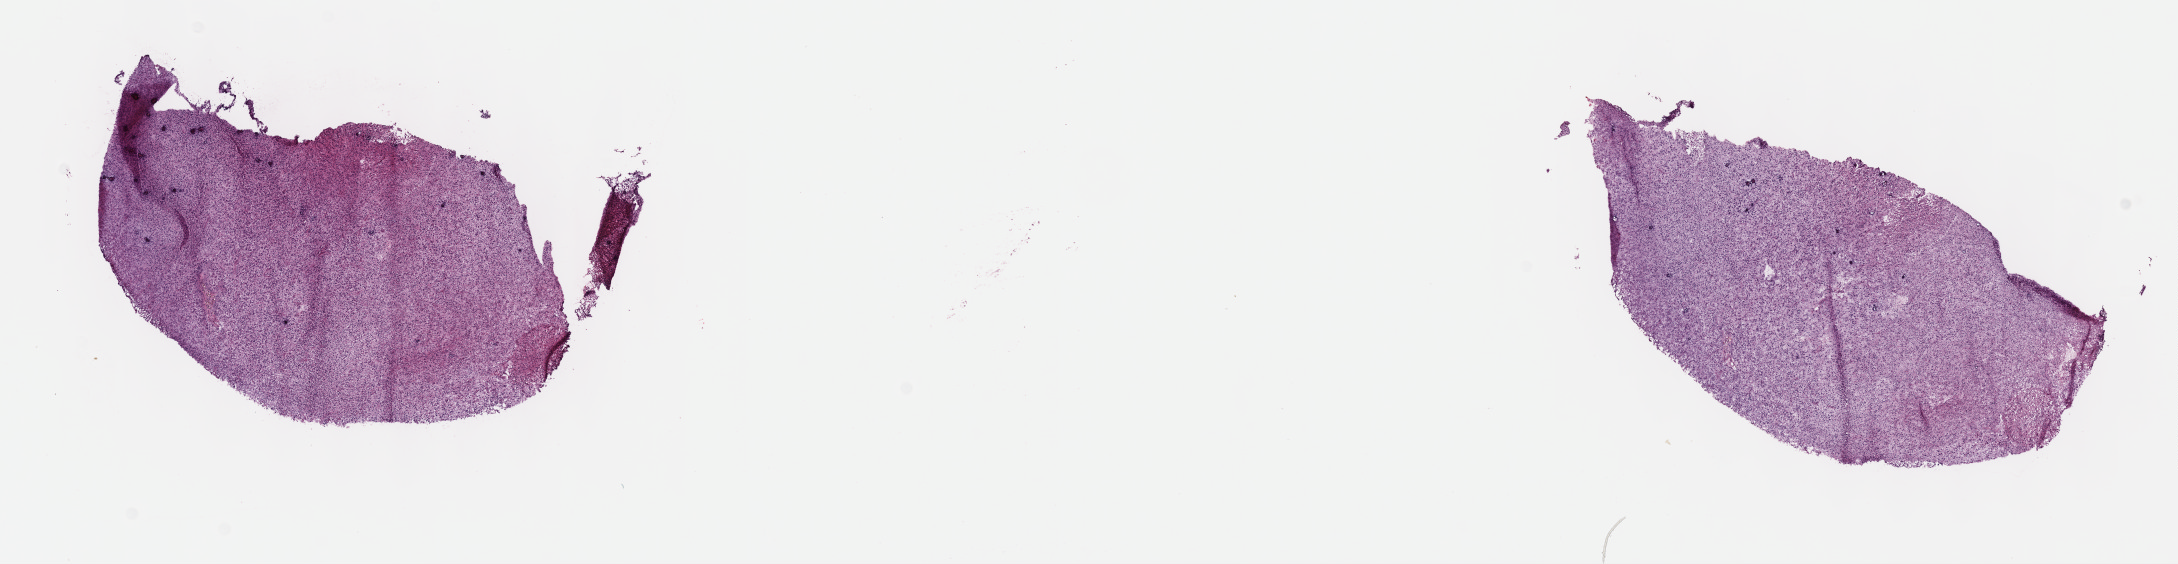
H&E-stained whole-slide image, whole scanned area (about 17.6 x 4.6 mm, slide scanned at 40x) shown as a low-resolution overview. Frozen section from the top of the tissue portion. Brain, primary tumour sample. Patient: male, age at initial diagnosis 55 years. Histologic grade: G3 (poorly differentiated). Pathologist review of this section (percent, as recorded): tumour cells 70%, tumour nuclei 90%, normal cells 10%, stromal cells 20%, necrosis 0%. Infiltration values recorded for this section: lymphocyte infiltration 0%, monocyte infiltration 0%, neutrophil infiltration 0%.
• pathologic diagnosis: Astrocytoma, anaplastic (cerebrum)